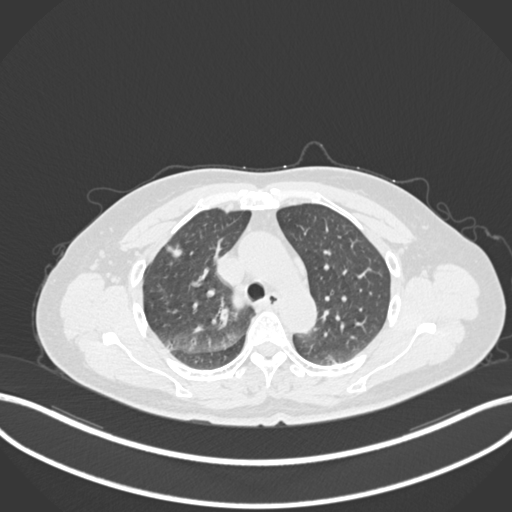
Chest CT, one axial slice; slice 164 of 223 in the series (ordered by position); reconstruction kernel B30f; lung window (W 1500 / L -600 HU); 1 mm slice thickness; 512 × 512 image matrix, field of view 400 × 400 mm. Female patient, age 56 years. From the clinical record (not read from this slice): clinical TNM (as recorded): T1c N0 M0.
Outlined on this slice (rectangle marked by the reading radiologist):
- lung tumour (recorded histology: adenocarcinoma): bounding box <163,237,186,261> (left, top, right, bottom; pixels)